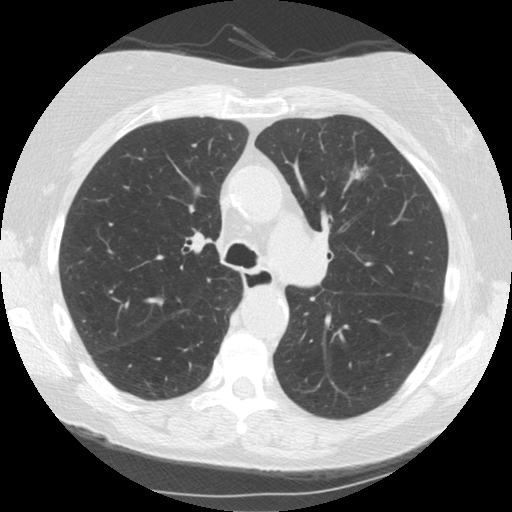
Low-dose screening chest CT, one axial slice; slice 98 of 153 in the series (ordered by position); 120 kVp; lung window (W 1500 / L -600 HU); 2.5 mm slice thickness; 512 × 512 image matrix, field of view 330 × 330 mm.
Annotated regions visible in this slice (outlined manually by an expert reader):
- lesion 1 (tumor, upper lobe of left lung): box from (x=351, y=169) to (x=362, y=180) px